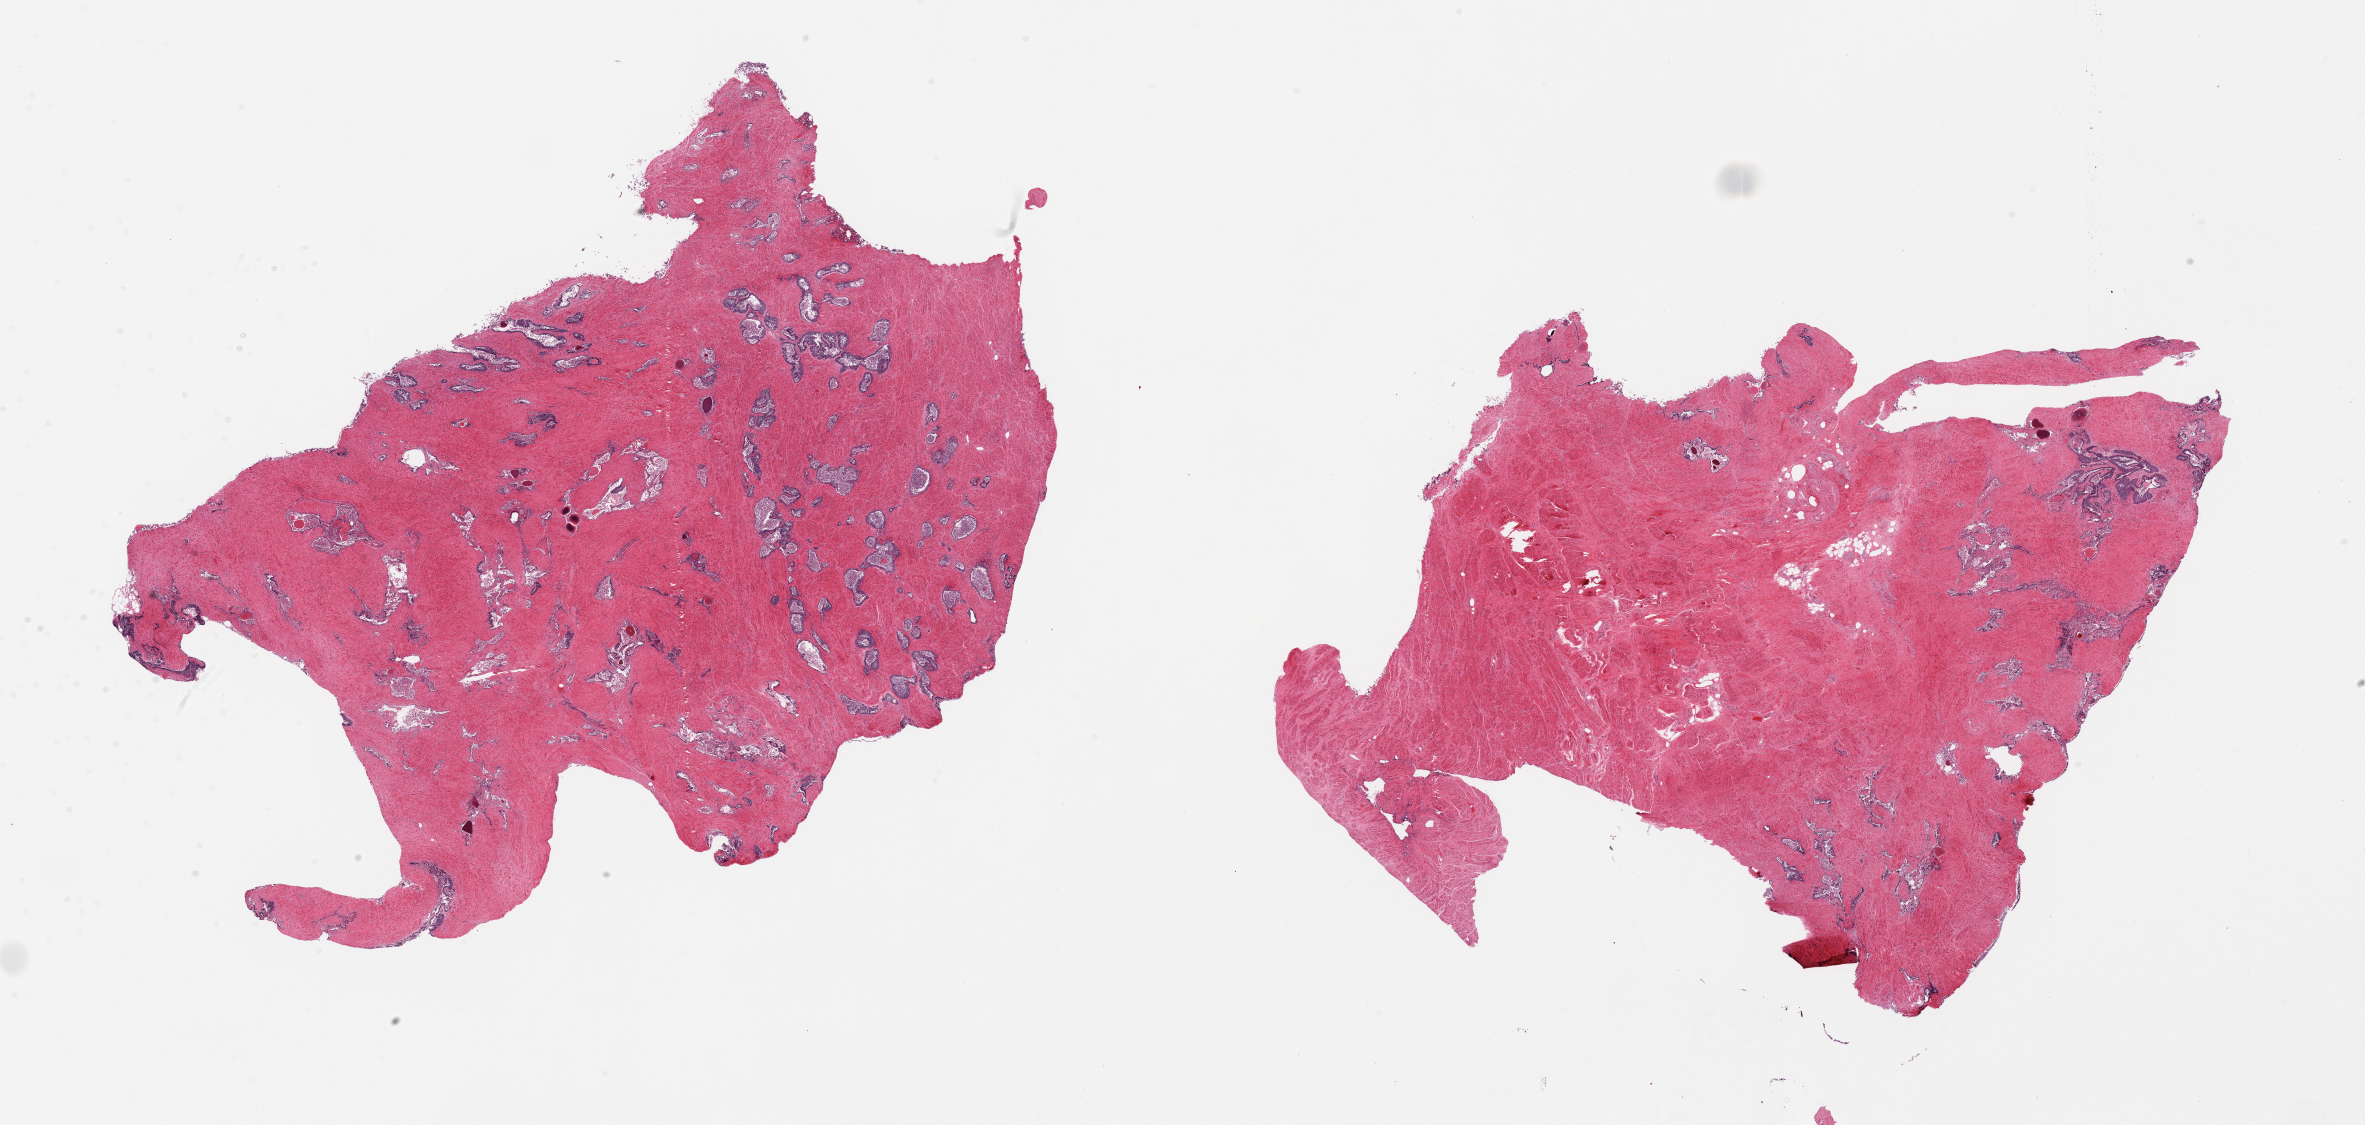
Hematoxylin and eosin (H&E) whole-slide image, a low-resolution overview of the entire scanned area, about 37.4 x 17.8 mm (from a 20x scan); PAXgene-fixed, paraffin-embedded tissue; target tissue: prostate; donor tissue sample.
* pathologist's review note for this sample: 2 pieces, glands confined to 20% of area in 1 piece, 2nd is evenly distributed, epithelium sloughing